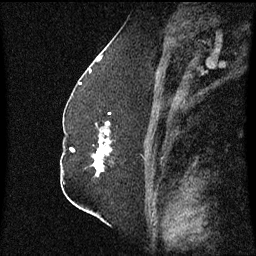
Breast MRI (dynamic contrast-enhanced), one sagittal slice. Position 33 of 60 along the scan axis. Dynamic contrast-enhanced series, image 2 of 3 at this slice position (ordered by acquisition). 1.5 T. TE 4.2 ms, TR 8.4 ms. 2.3 mm slice thickness. 256 × 256 image matrix. Patient: female, 52 years. Case-level facts recorded for this patient, not image findings: setting: breast cancer imaged before/during neoadjuvant chemotherapy; receptor status: HR-positive, HER2-negative.
Outlined on this slice (semi-automatically segmented with operator editing):
- analysis volume of interest (the breast-tissue region the enhancement analysis was run in; not a lesion): bounding box [x1, y1, x2, y2] px = [93, 114, 112, 177]
- tumour enhancement mask (voxels above the 70 % enhancement threshold inside the analysis volume of interest): [93, 122, 111, 175]